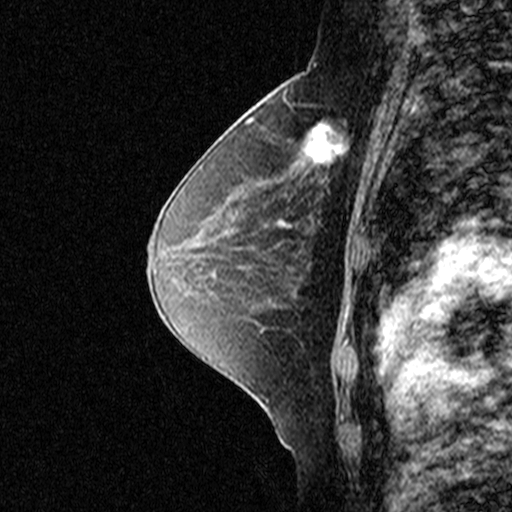
Breast MRI (dynamic contrast-enhanced), one sagittal slice; position 24 of 44 along the scan axis; dynamic contrast-enhanced study with each time point stored as its own series, time point 2 of 3 at this slice position (early post-contrast, ordered by acquisition time); 1.5 T; TE 4.5 ms, TR 11 ms; 512 × 512 image matrix, field of view 200 × 200 mm. Patient: female, 49 years. From the clinical record (not read from this slice): setting: breast cancer imaged before/during neoadjuvant chemotherapy; receptor status: triple-negative.
Outlined on this slice (semi-automatic segmentation, software-assisted and operator-edited):
- analysis volume of interest (the breast-tissue region the enhancement analysis was run in; not a lesion): bounding box [x1, y1, x2, y2] px = [276, 94, 369, 181]
- tumour enhancement mask (voxels above the 90 % enhancement threshold inside the analysis volume of interest): [307, 127, 328, 161]